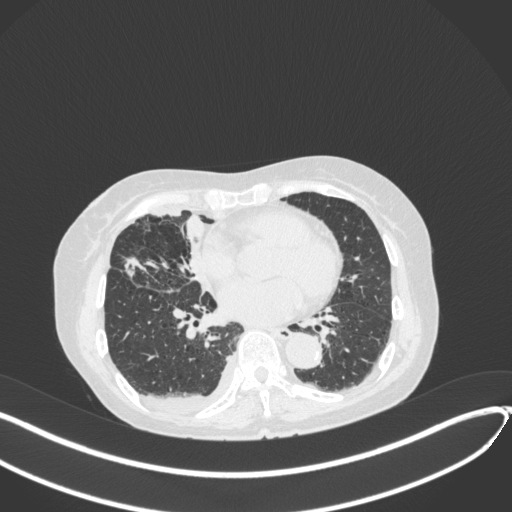
Chest CT, one axial slice. Slice 168 of 418 in the series (ordered by position). Reconstruction kernel B31f. 120 kVp. Lung window (W 1500 / L -600 HU). 1 mm slice thickness. 512 × 512 image matrix, field of view 400 × 400 mm. Patient: female, 75 years. From the clinical record (not read from this slice): clinical TNM (as recorded): T2a N3 M0.
Outlined on this slice (bounding box drawn by a radiologist):
- lung tumour (recorded histology: adenocarcinoma): bounding box [x1, y1, x2, y2] px = [119, 247, 143, 279]